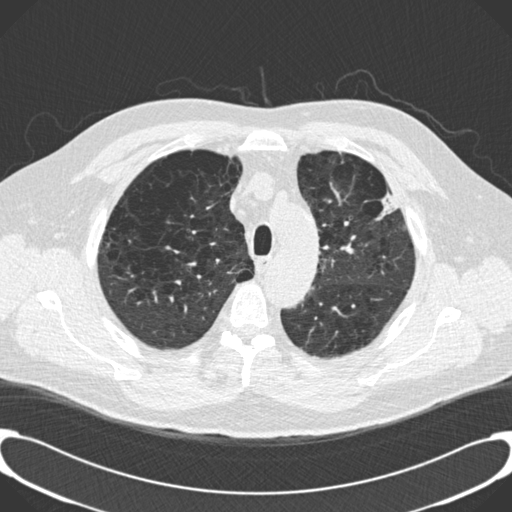
Low-dose screening chest CT, axial slice; third screening round (two years after baseline); lung window (W 1500 / L -600 HU); 512 × 512 image matrix. Male, age 59 years at enrolment. Current smoker at enrolment.
• Expert reader's lesion annotation, bounding box [x1, y1, x2, y2] px = [362, 171, 411, 228].
• No non-calcified nodule or mass ≥4 mm was recorded by the screening reader at this exam.
• Later outcome: lung cancer diagnosed 134 days after this screen — bronchiolo-alveolar carcinoma, mixed mucinous and non-mucinous, left upper lobe, stage IA (AJCC 6th edition), 20 mm at pathology.